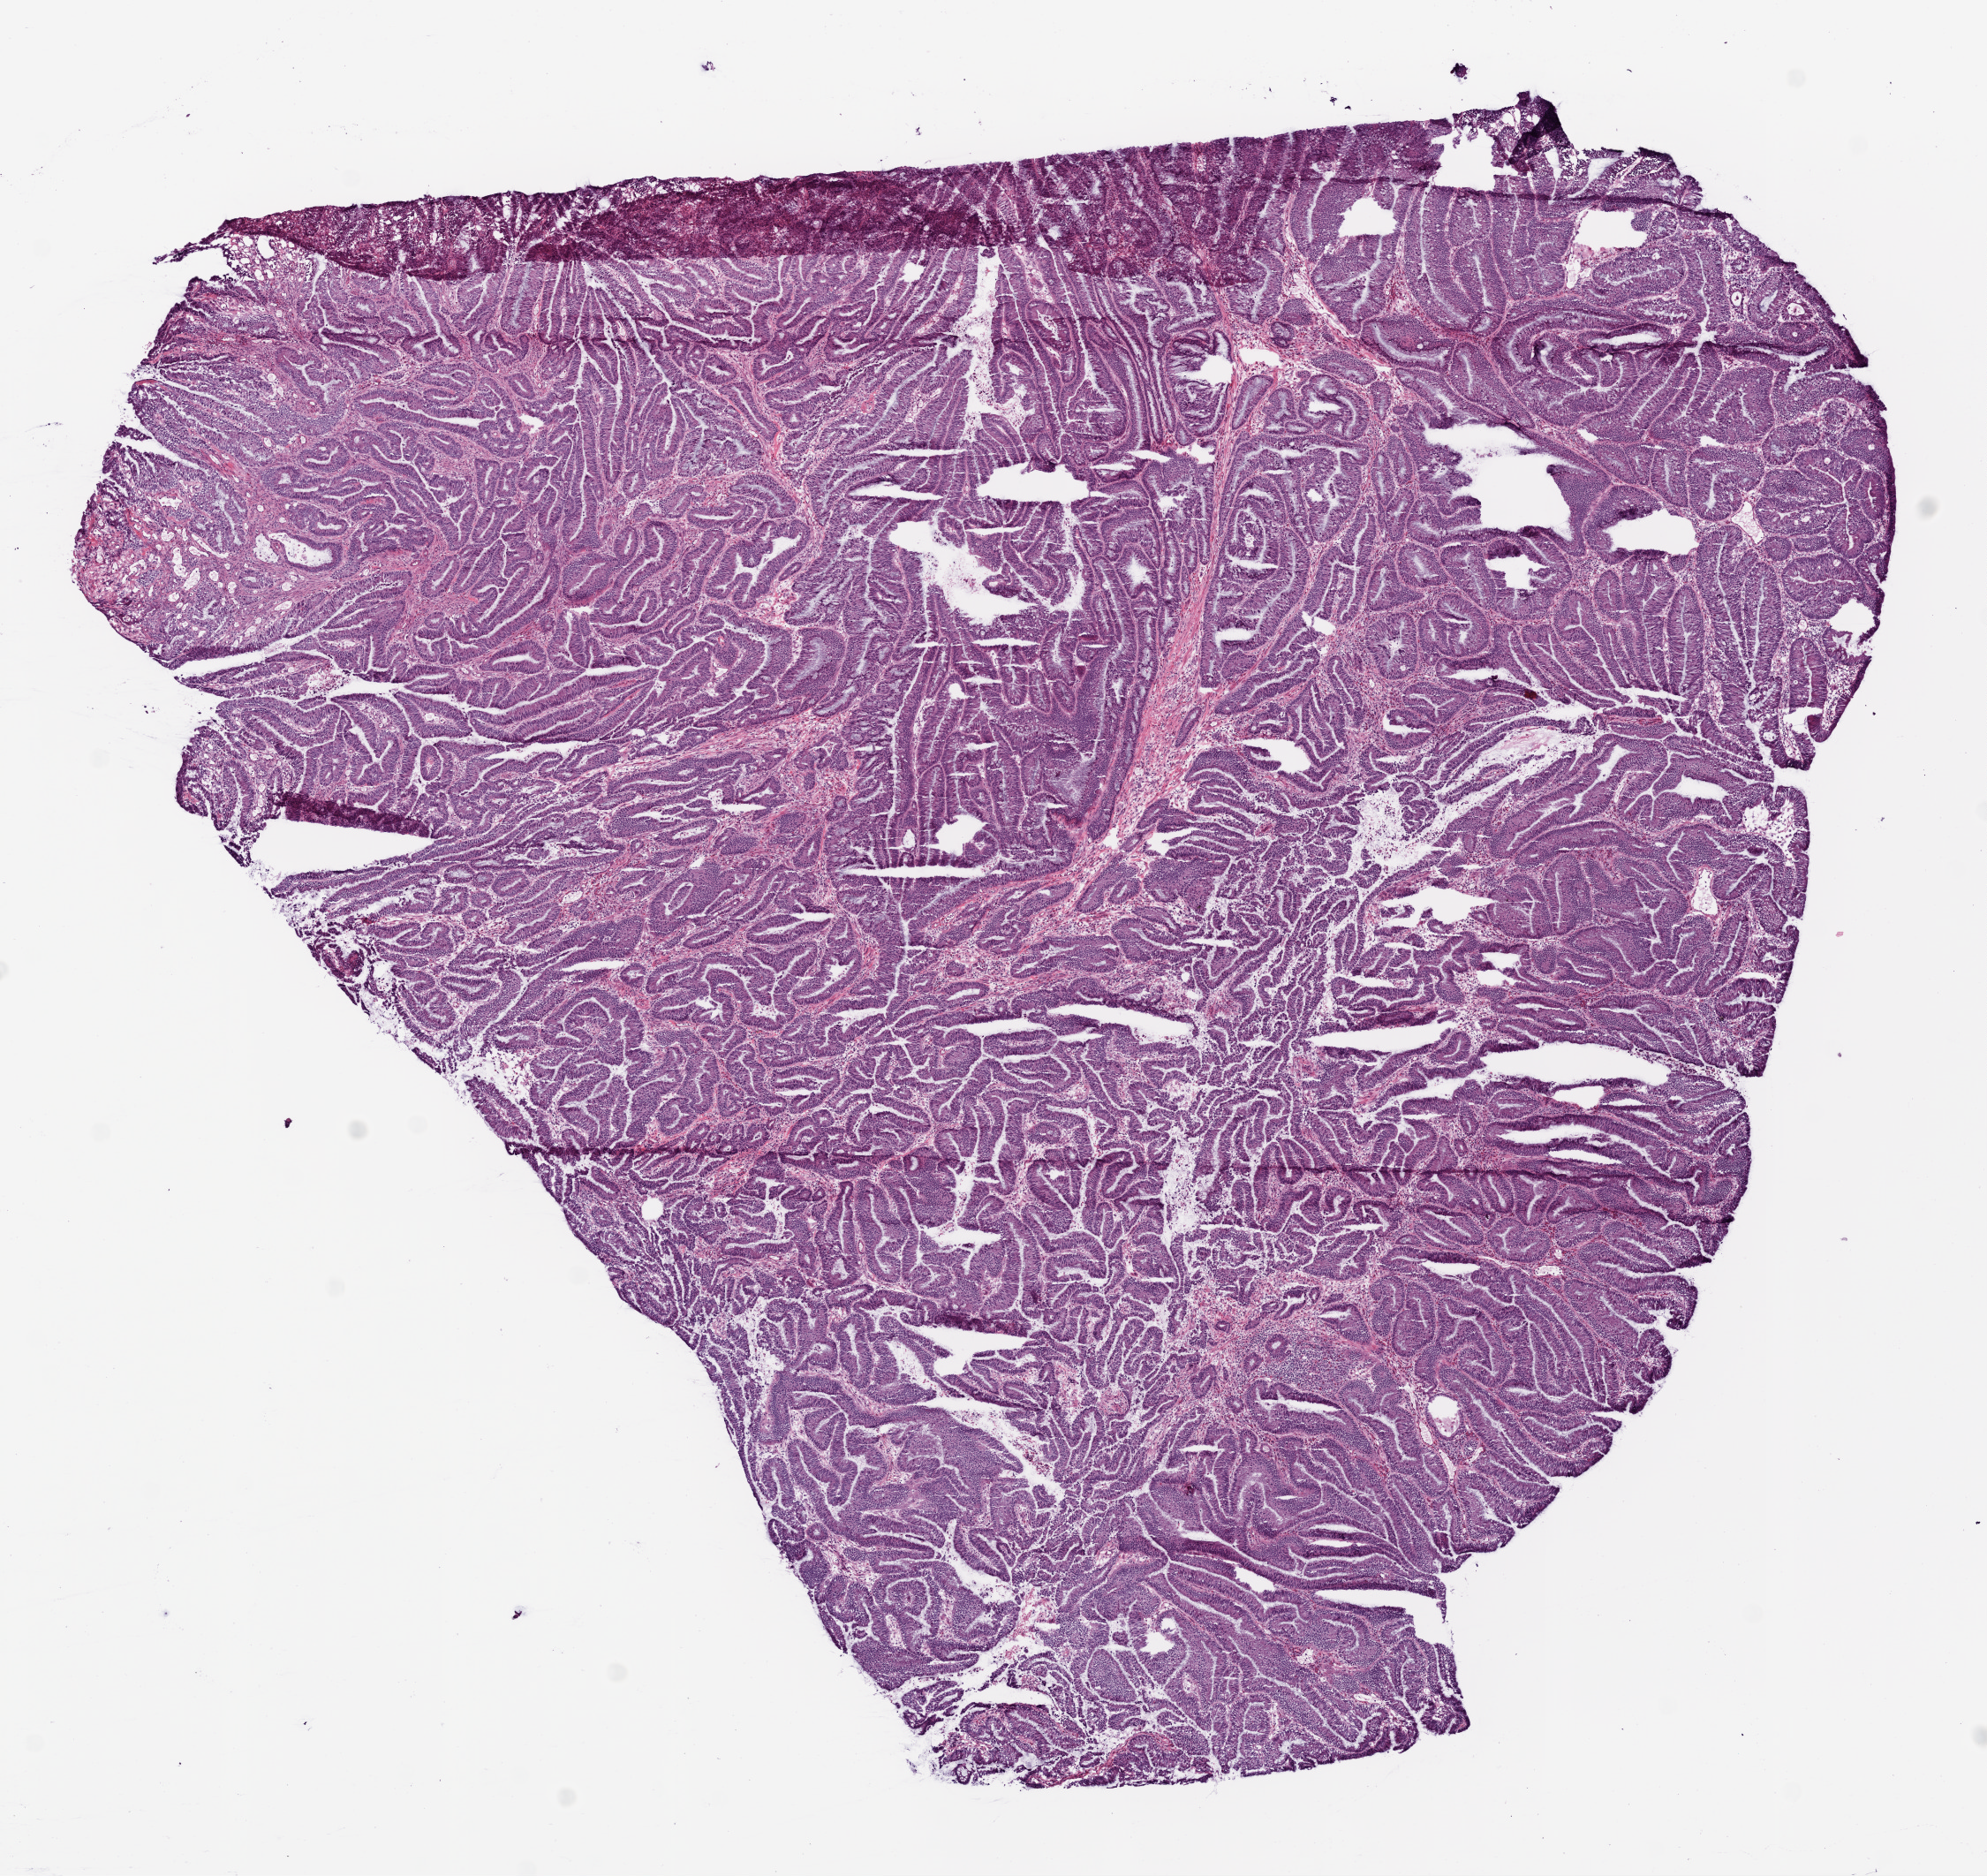
H&E-stained whole-slide image, a low-resolution overview of the entire scanned area, about 9.0 x 8.5 mm. Frozen section from the bottom of the tissue portion. Sample: primary tumour, rectum. Male patient; age at initial diagnosis 72 years.
Diagnosis: Adenocarcinoma, NOS (rectosigmoid junction).